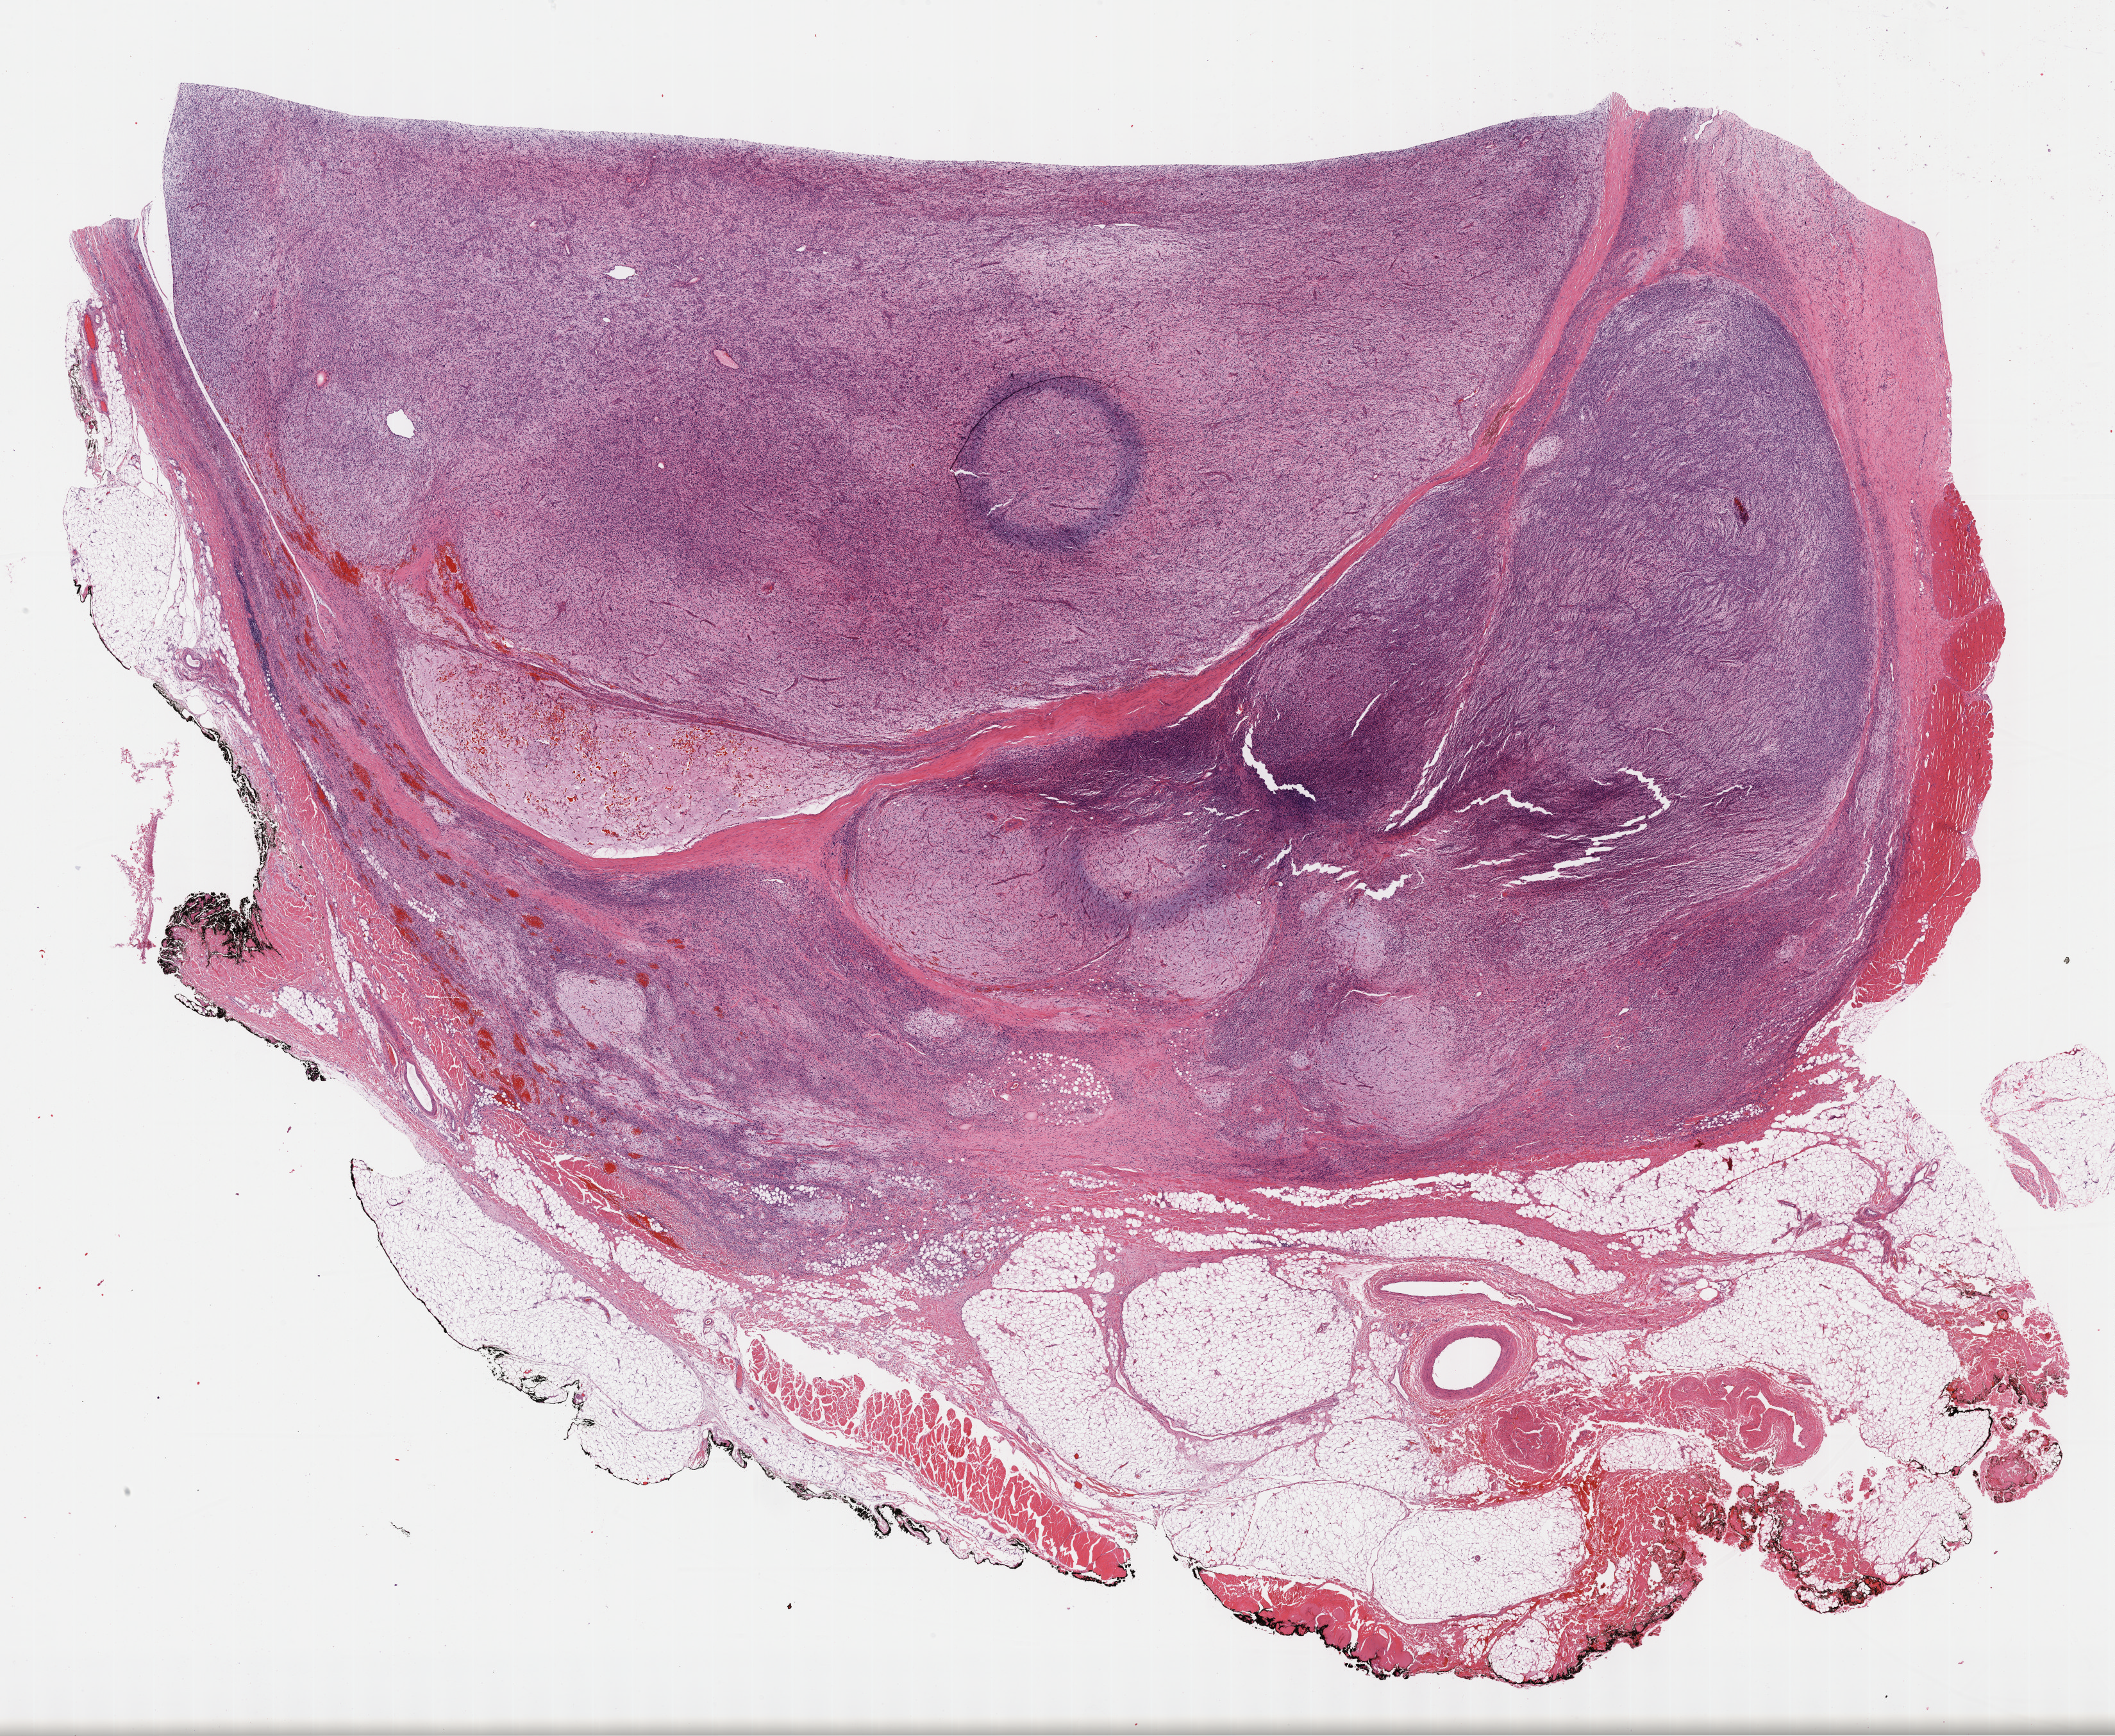
Whole-slide histology image, H&E — shown as a low-resolution overview of the whole scanned area (about 26.7 x 21.9 mm, from a 40x scan); formalin-fixed paraffin-embedded (FFPE) diagnostic section; connective, subcutaneous and other soft tissues, primary tumour sample. Patient: male, age at initial diagnosis 35 years.
- histologic diagnosis: Fibromyxosarcoma (connective, subcutaneous and other soft tissues of lower limb and hip)